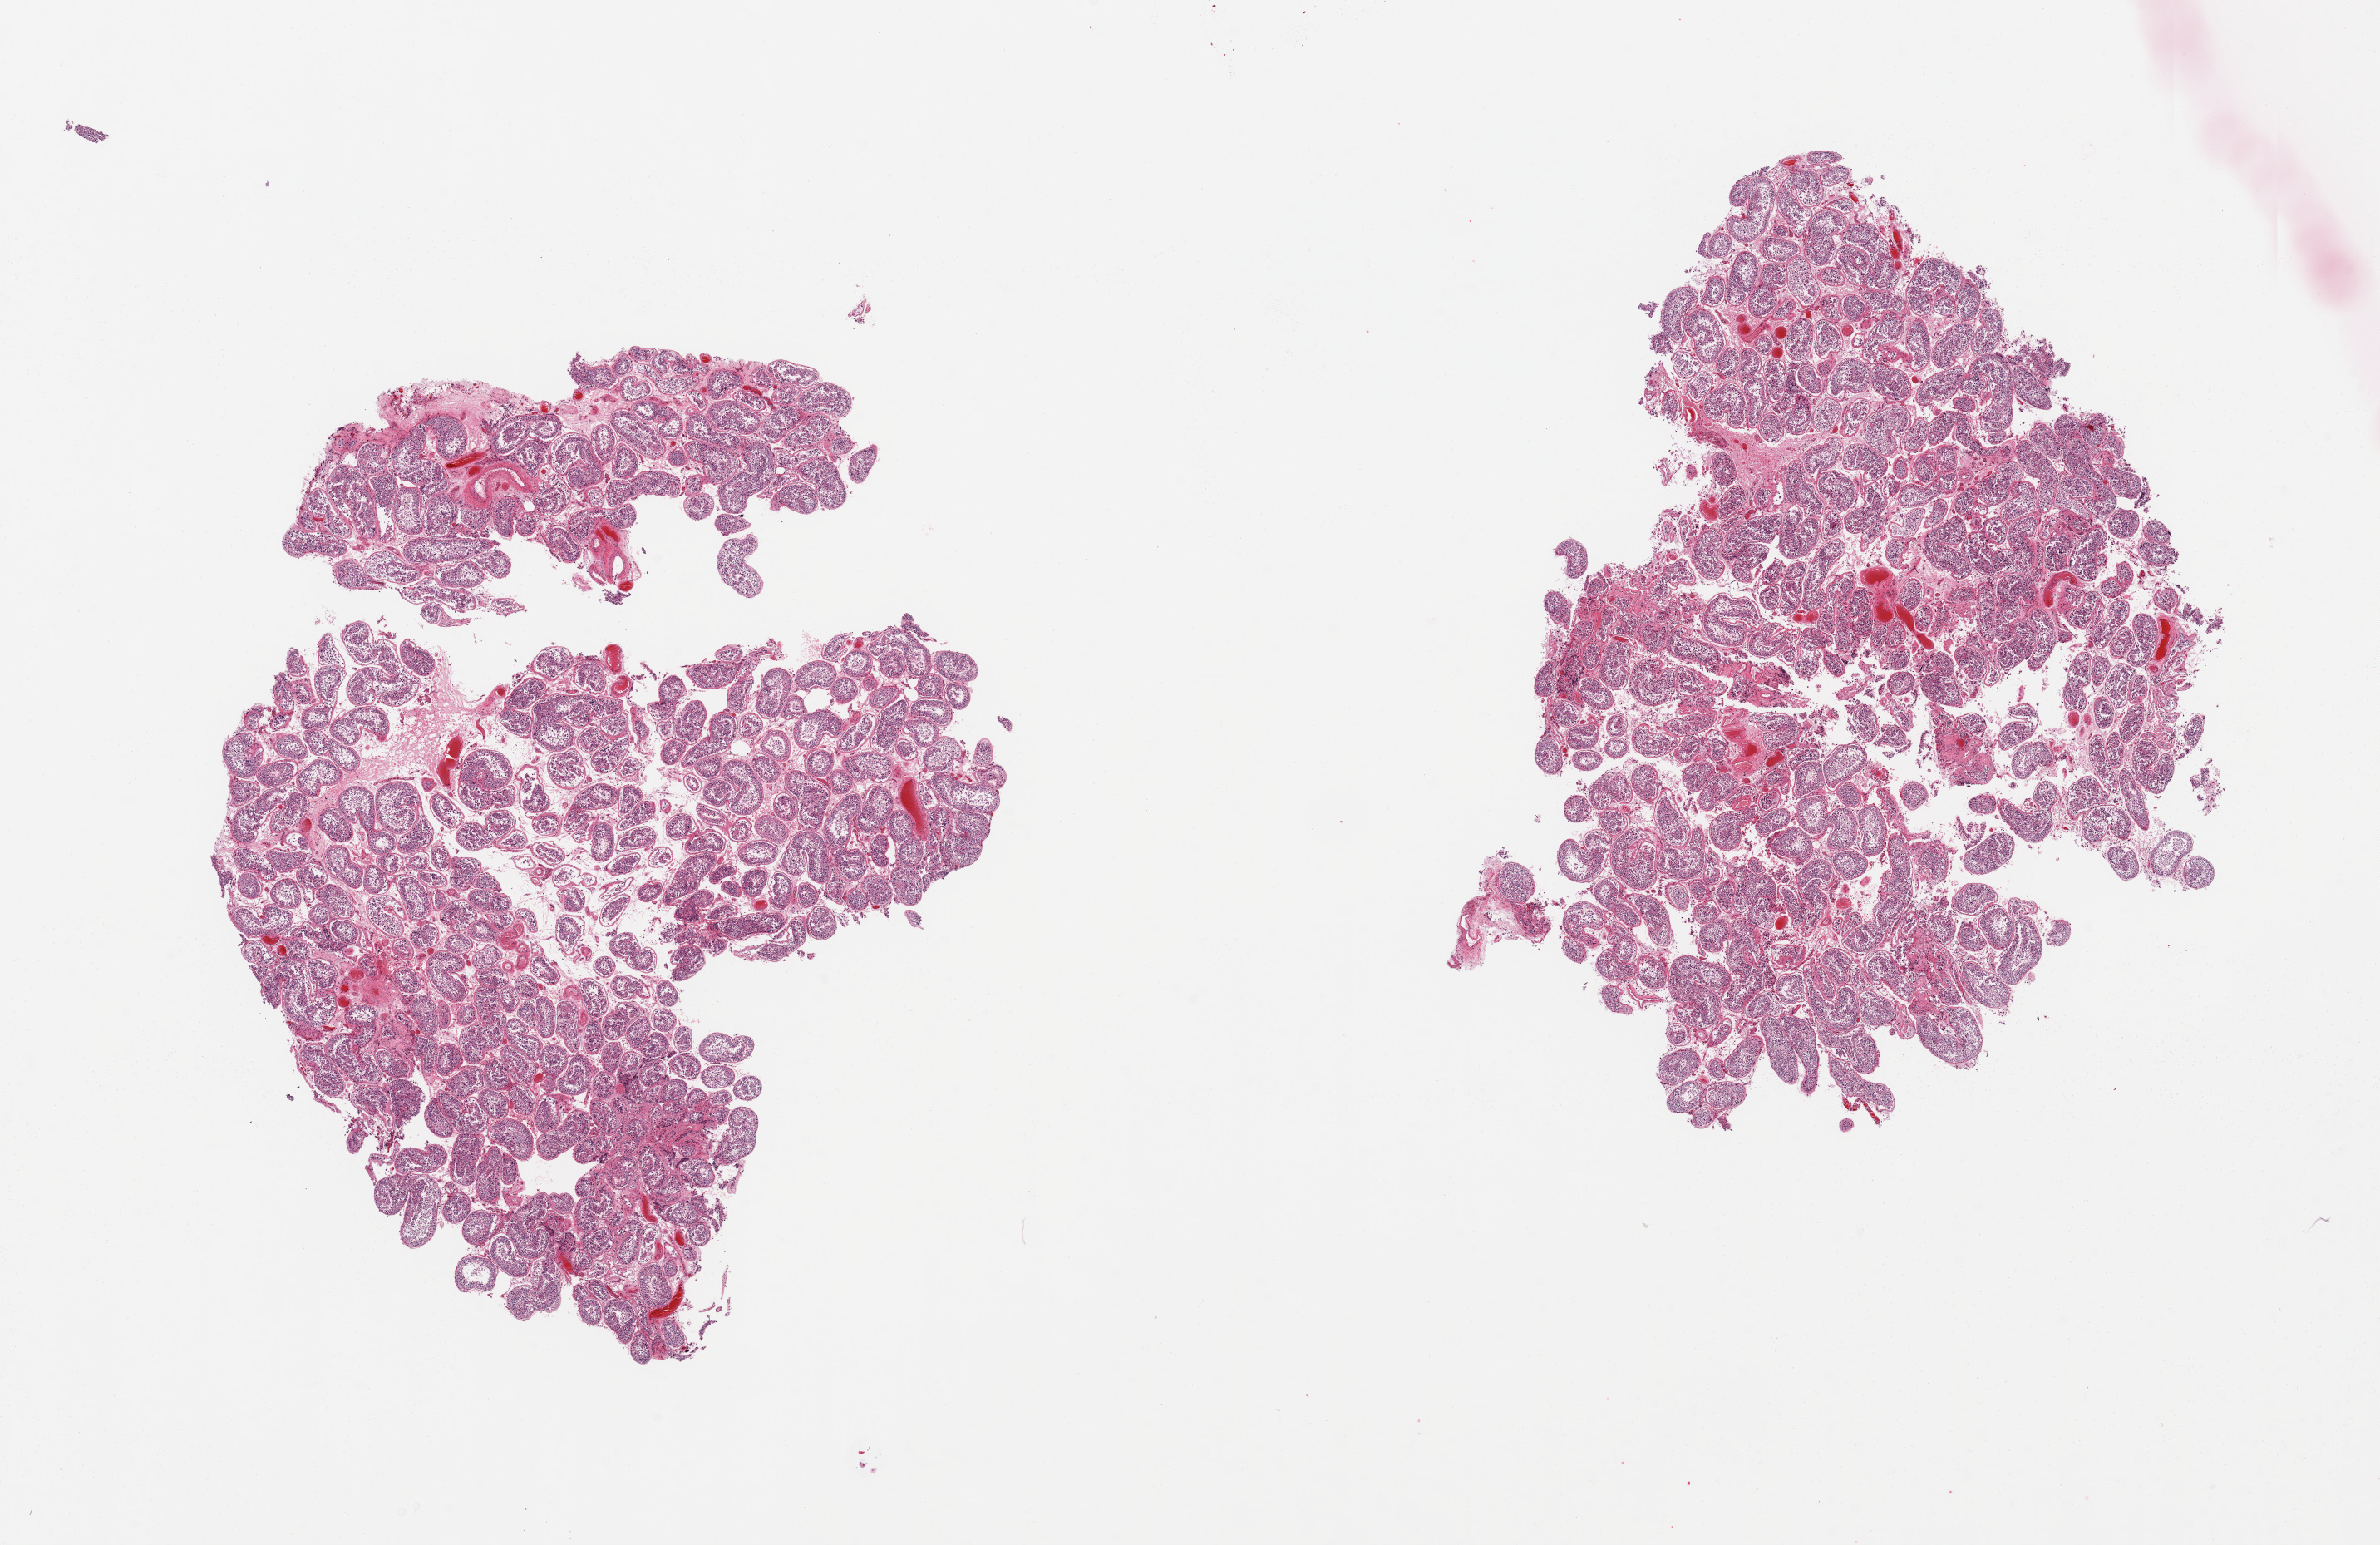
Whole-slide image, haematoxylin and eosin stain, brightfield — low-resolution overview of the scanned area, about 22.6 x 14.7 mm (from a 20x scan). PAXgene-fixed paraffin-embedded (PFPE) section. Section of testis (target tissue). Donor tissue sample. Donor sex: male.
• reviewer comment on this tissue sample: 2 pieces; spermatogenesis preserved; congestion